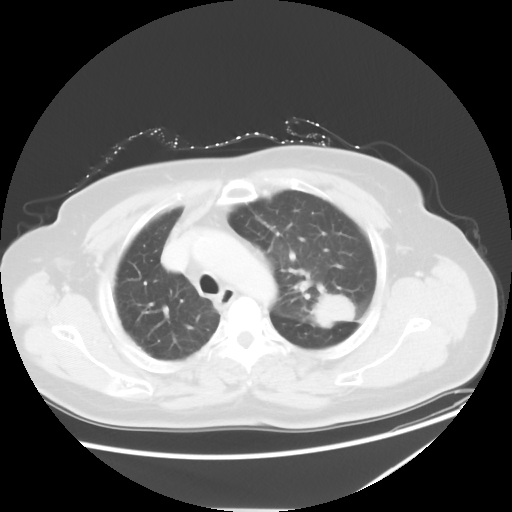
Chest CT, one axial slice. Reconstruction kernel STANDARD. 120 kVp. Lung window (W 1500 / L -600 HU). 5 mm slice thickness. 512 × 512 image matrix, field of view 384 × 384 mm. Patient: female, 61 years. From the clinical record (not read from this slice): clinical TNM (as recorded): T1c N3 M1.
Outlined on this slice (rectangle marked by the reading radiologist):
- lung tumour (recorded histology: adenocarcinoma): bounding box <304,289,360,332> (left, top, right, bottom; pixels)